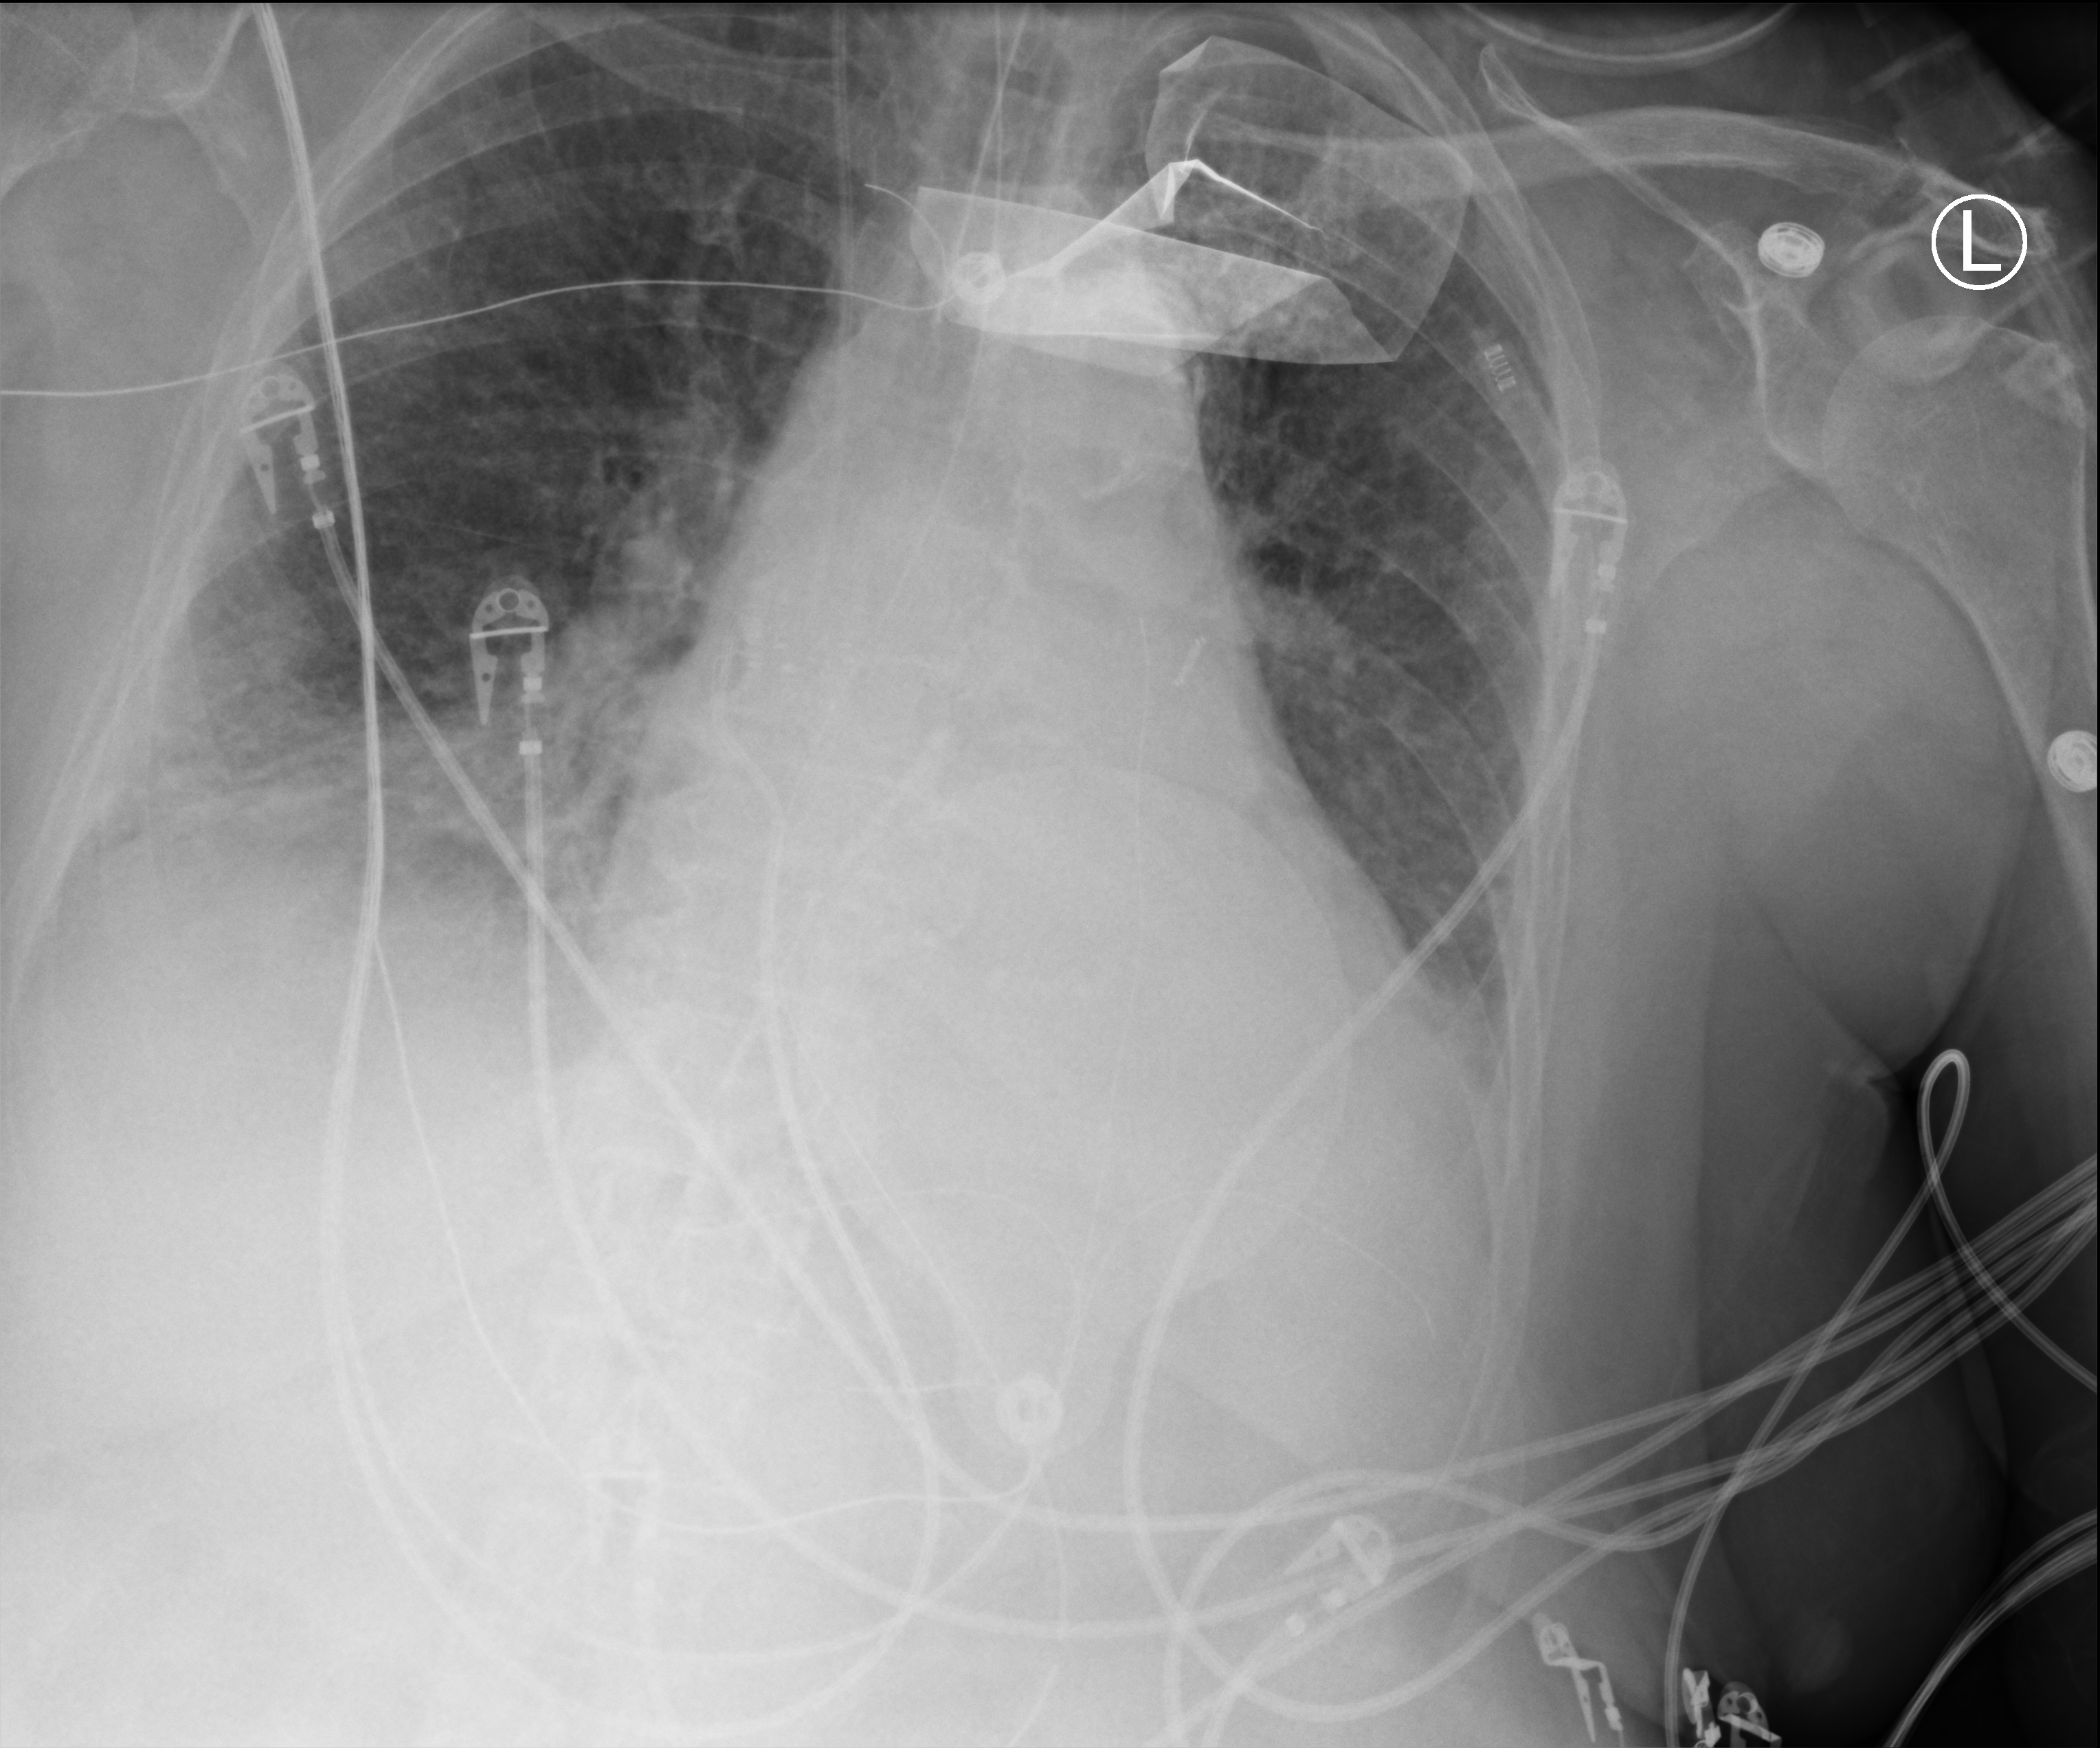
Bedside chest radiograph (computed radiography), anteroposterior (AP) projection. Female patient hospitalised with COVID-19, age 75–90 years.
Hospital-stay facts (about this admission, not read from this image; timing relative to this image not recorded): COPD (admission record): yes; admitted to intensive care during this hospital stay: yes.